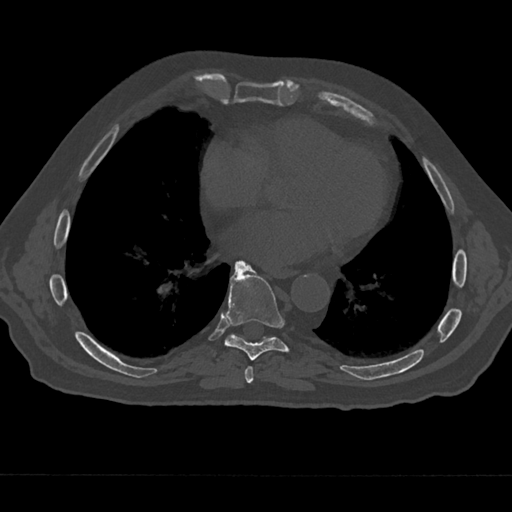
CT including the spine, one axial slice; slice 310 of 797 in the series (ordered by position); 120 kVp; bone window (W 1800 / L 400 HU); 512 × 512 image matrix. Patient: male, 75 years. From the clinical record (not read from this slice): primary cancer: renal; vertebrae with lytic lesions (as recorded): T4.
Annotated regions visible in this slice (semi-automatically segmented with operator editing):
- T7 vertebra: bounding box <238,366,254,384> (left, top, right, bottom; pixels)
- T8 vertebra: <213,261,290,360>